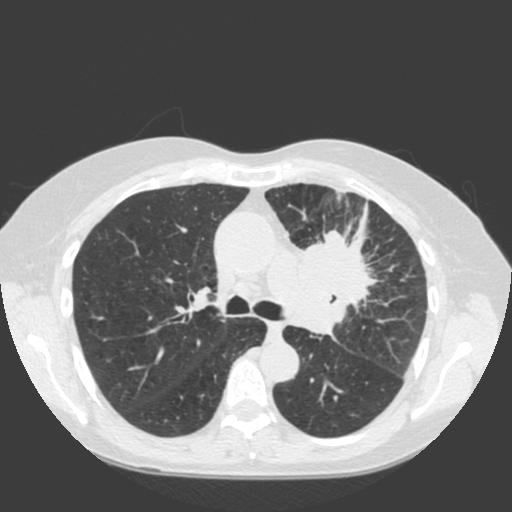
Chest CT (low-dose screening protocol), one axial image, baseline annual screen, lung window (W 1500 / L -600 HU). Female participant, aged 66 years at enrolment. Current smoker at enrolment.
• Expert-annotated lung lesion, bounding box [x1, y1, x2, y2] px = [280, 219, 399, 326].
• The exam's reader record, not a measurement of the box and not confirmed to be the same lesion: non-calcified nodule or mass ≥4 mm, left upper lobe, 61 × 45 mm, spiculated (stellate) margins, soft tissue attenuation.
• Official screen result: positive, change unspecified: nodule(s) >= 4 mm or enlarging nodule(s), mass(es), or other non-specific abnormalities suspicious for lung cancer.
• Lung cancer was diagnosed 19 days after this screen: squamous cell carcinoma, keratinizing, NOS, left upper lobe, left hilum, mediastinum, left main stem bronchus, other location, poorly differentiated (G3), stage IIIB (AJCC 6th edition), 60 mm at pathology.